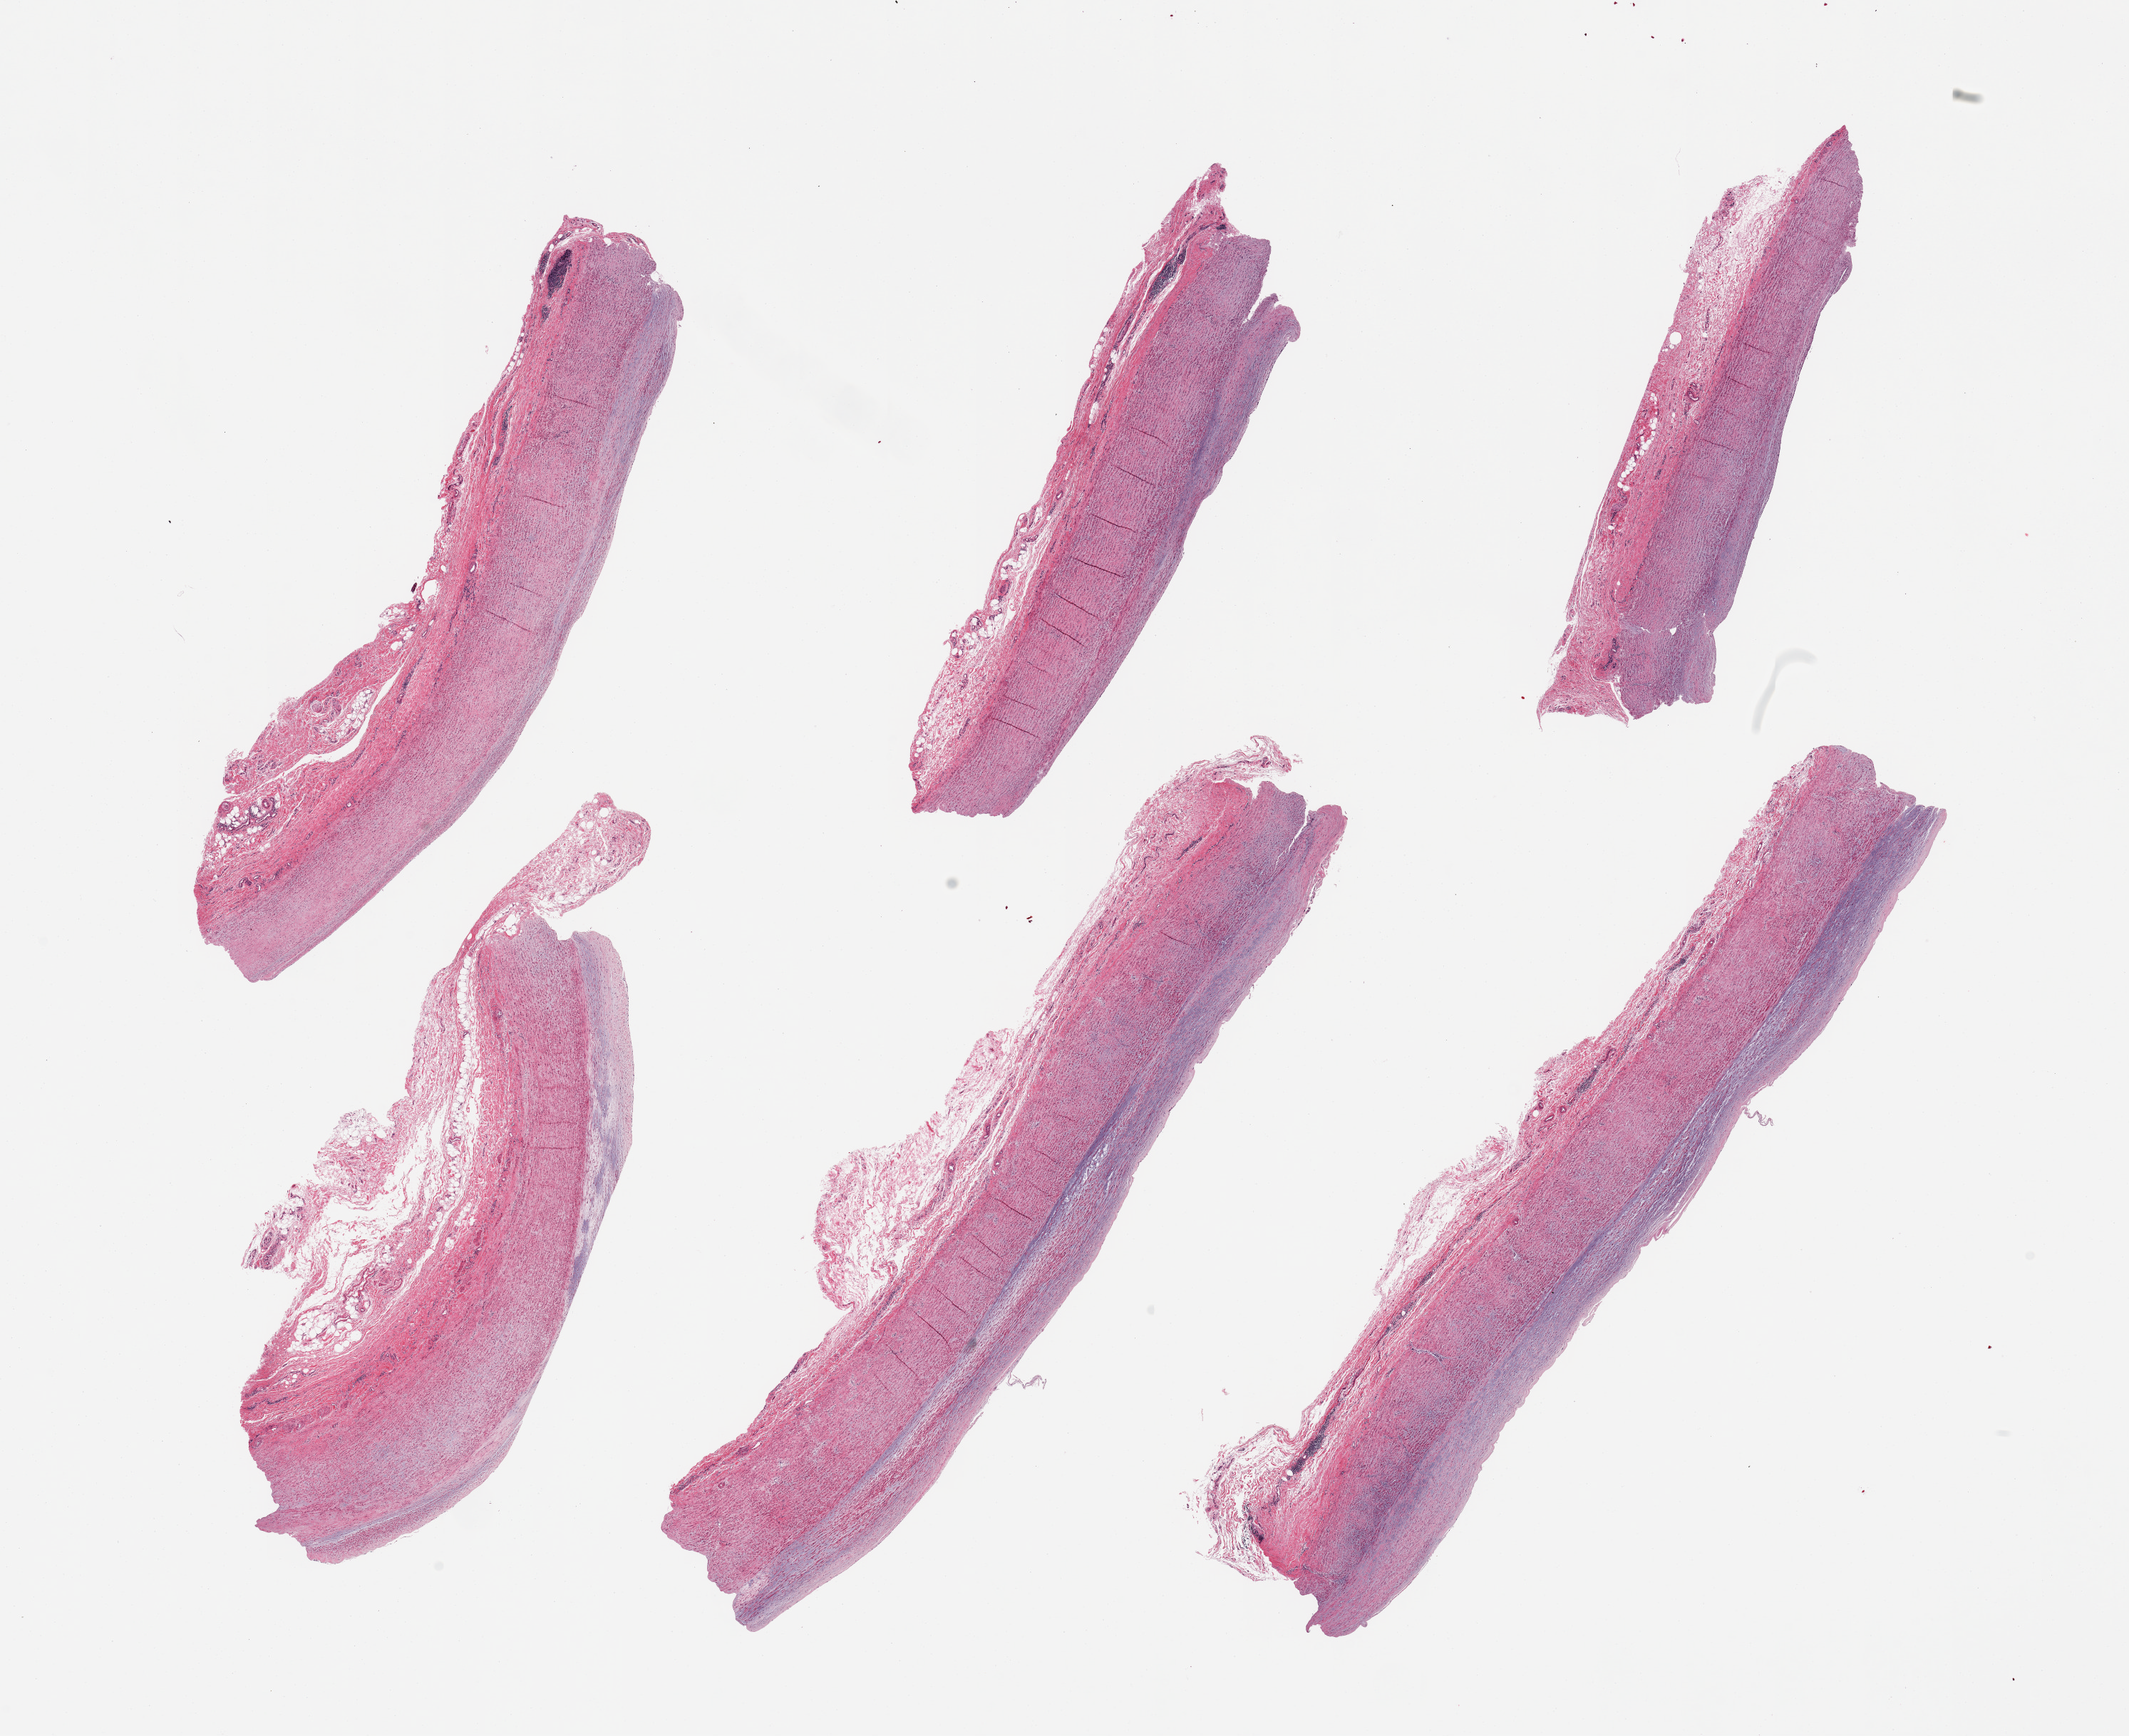
Whole-slide image, haematoxylin and eosin stain, a low-resolution overview of the entire scanned area, about 23.6 x 19.3 mm, PAXgene-fixed, paraffin-embedded tissue, section of aorta (target tissue), tissue donor sample. Donor: female.
Pathologist's review note for this sample: 6 pieces, atherosis up to ~0.7mm.